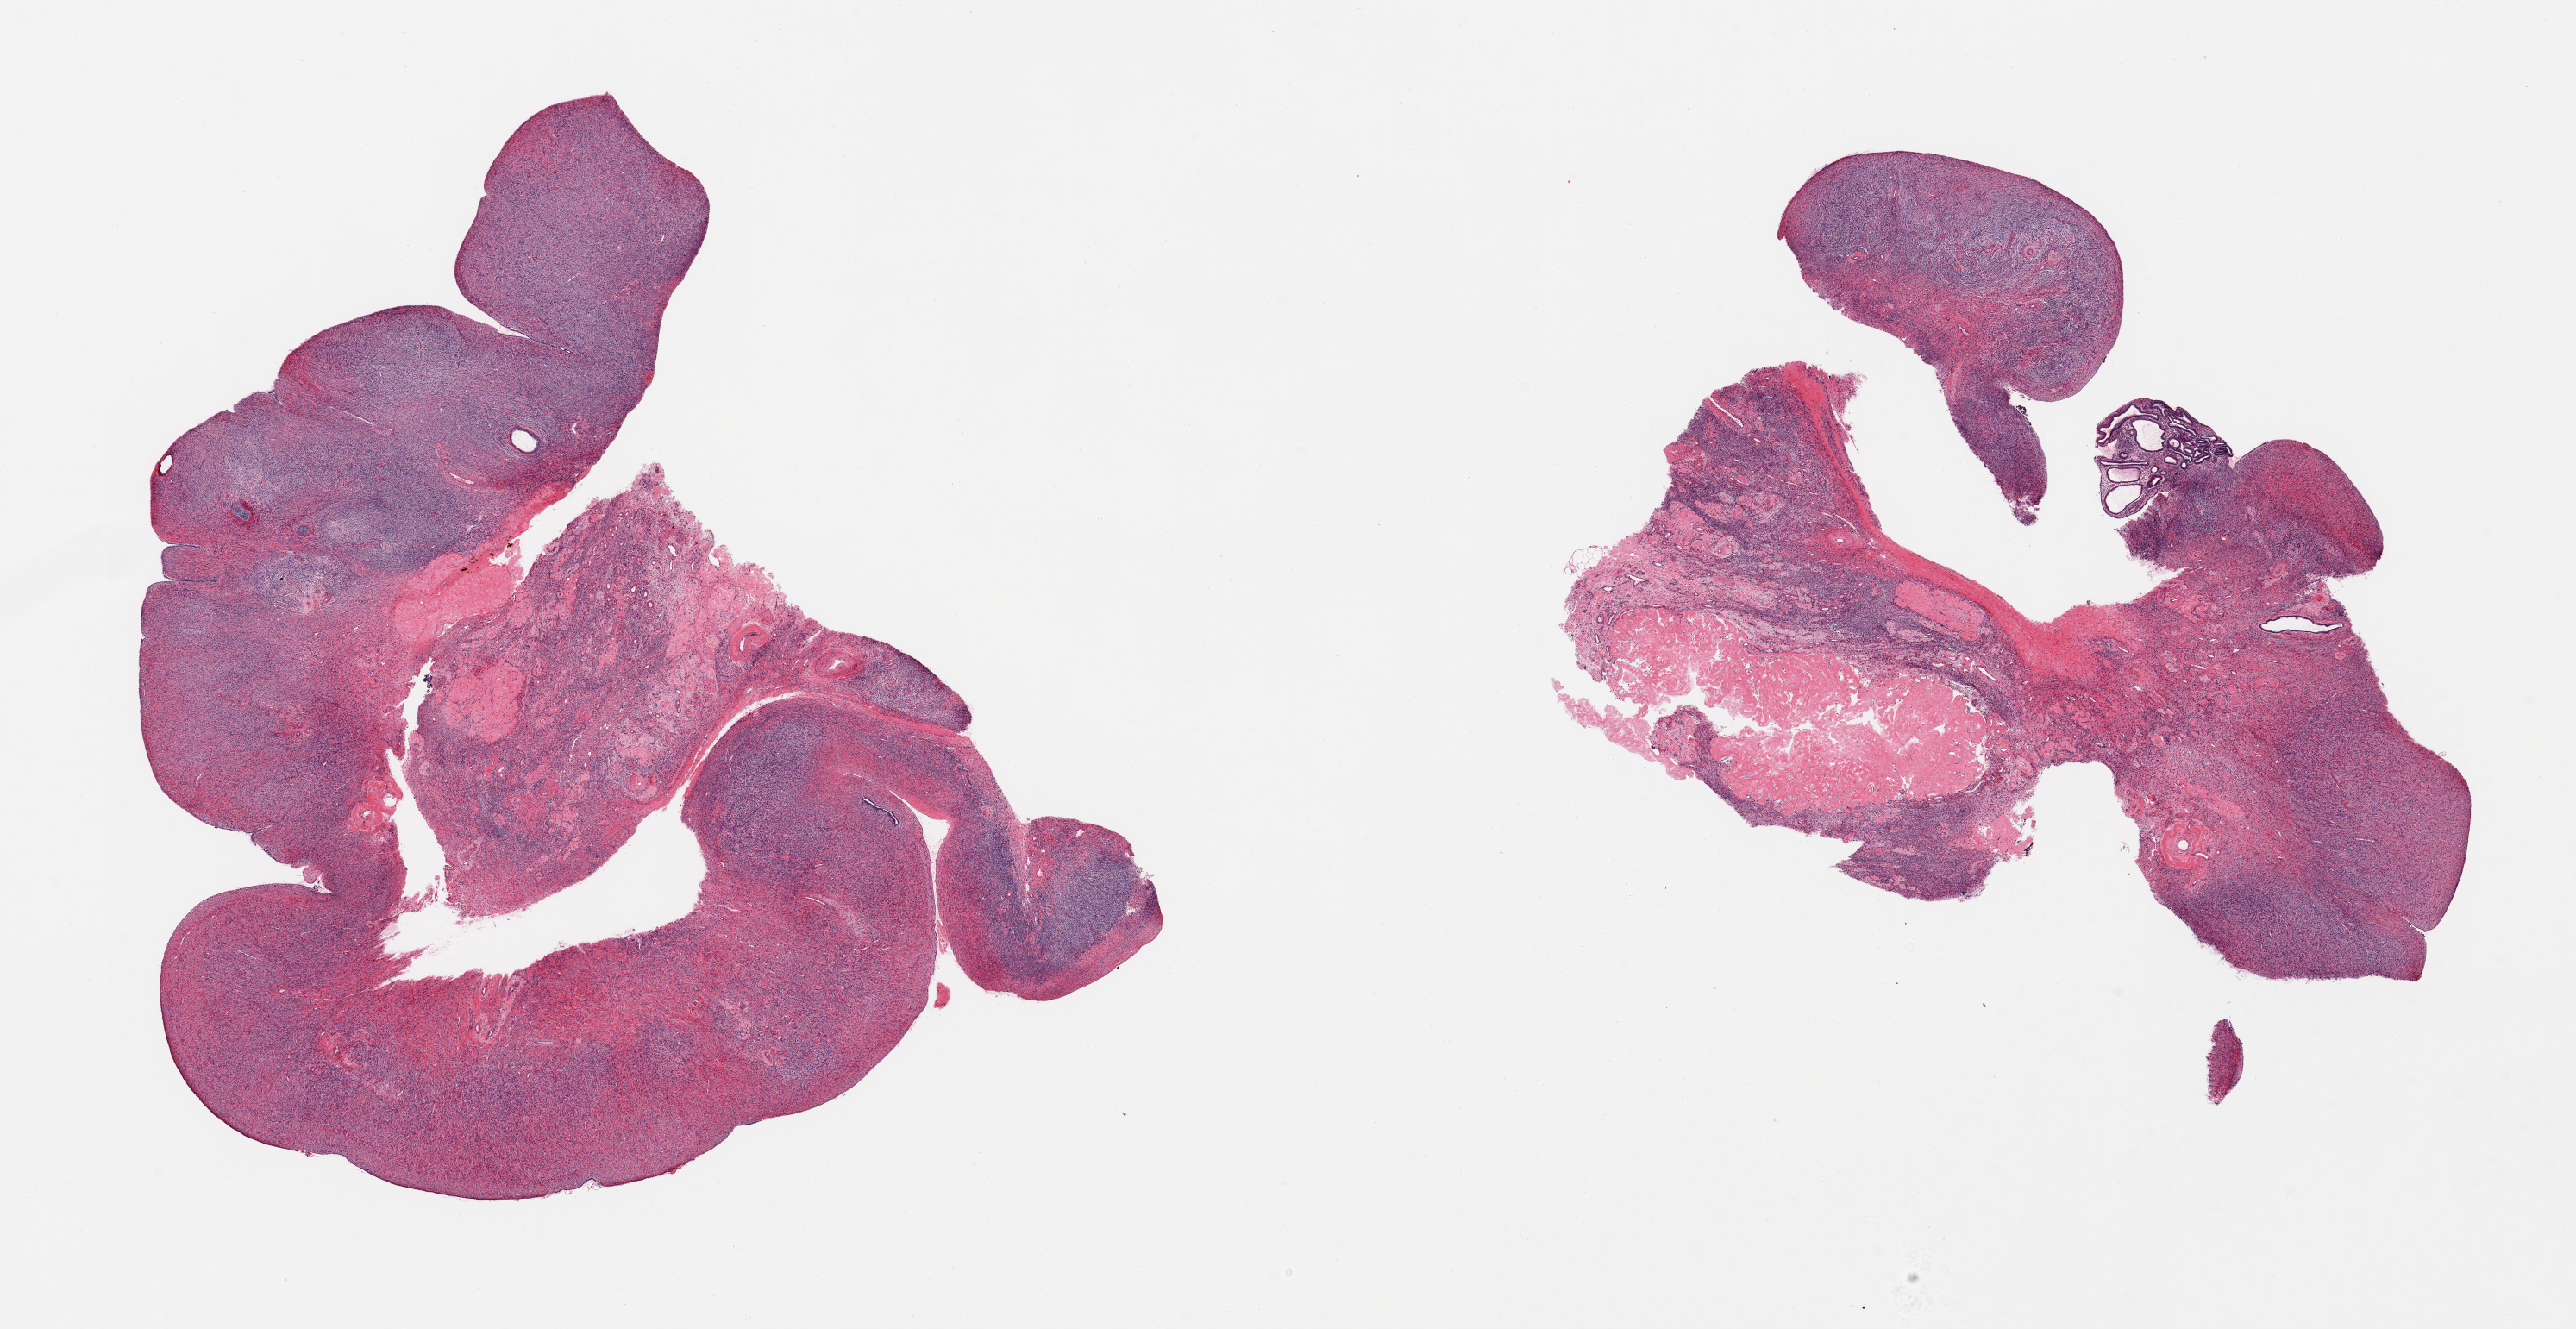
Whole-slide image, hematoxylin and eosin (H&E) stain, whole scanned area (about 23.6 x 12.2 mm, acquisition: 20x scan) shown as a low-resolution overview; PAXgene-fixed, paraffin-embedded tissue; sampled site (target tissue): ovary; donor tissue sample. Donor sex: female.
- review note (as recorded): 2 pieces; atrophic; corpora albicantia; small focus of endometriosis